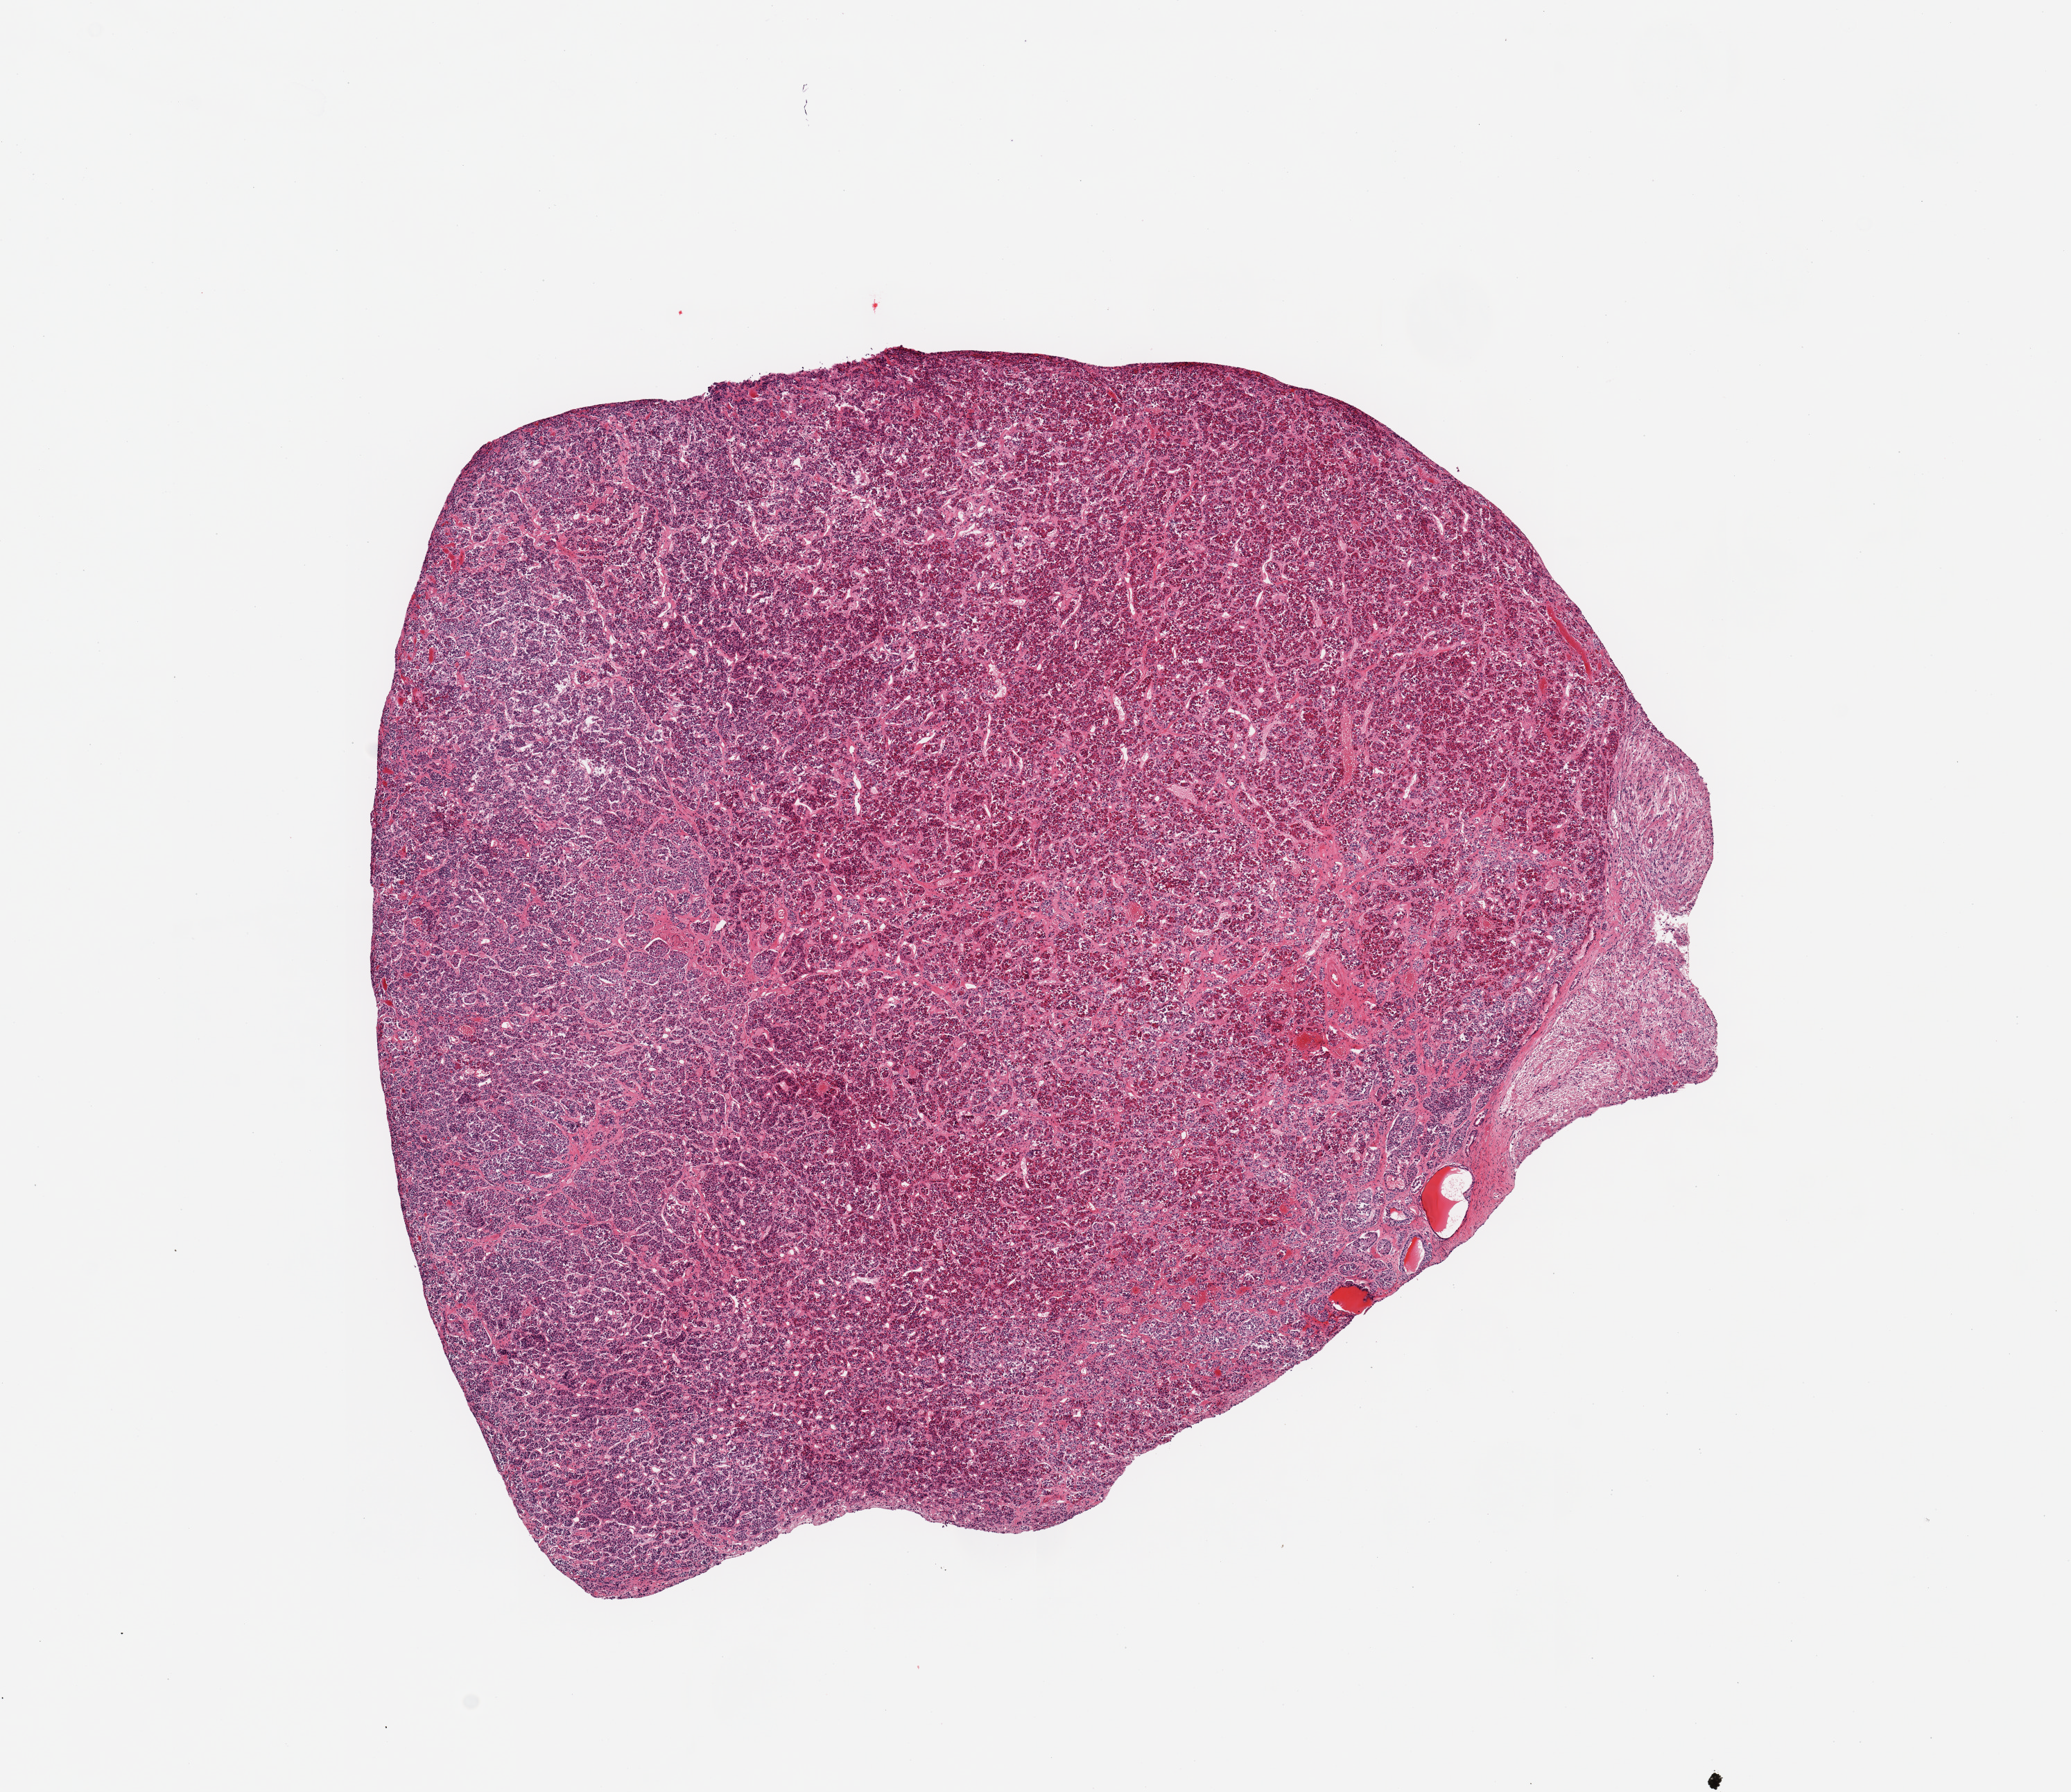
Haematoxylin and eosin whole-slide image, a low-resolution overview of the entire scanned area, about 11.8 x 10.2 mm (from a 20x scan), PAXgene-fixed paraffin-embedded (PFPE) section, target tissue: pituitary, tissue donor sample. Male donor.
Reviewer comment on this tissue sample: 1 piece, mainly adenohpophysis, ~2x1mm nubbin of neurohypophysis.